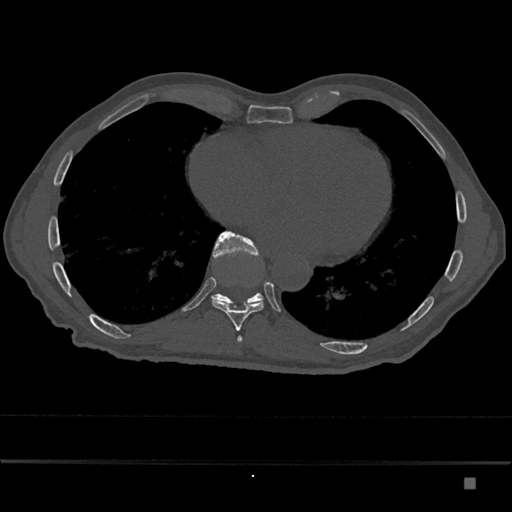
CT including the spine, one axial slice; position 784 of 797 along the scan axis; reconstruction kernel Br40s/3; bone window (W 1800 / L 400 HU); 0.5 mm slice thickness; 512 × 512 image matrix, field of view 390 × 390 mm. Patient: male, 72 years. From the clinical record (not read from this slice): primary cancer: prostate.
Structures marked on this image (semi-automatically segmented with operator editing):
- T10 vertebra: bounding box <211,231,264,307> (left, top, right, bottom; pixels)
- T9 vertebra: <211,300,264,331>